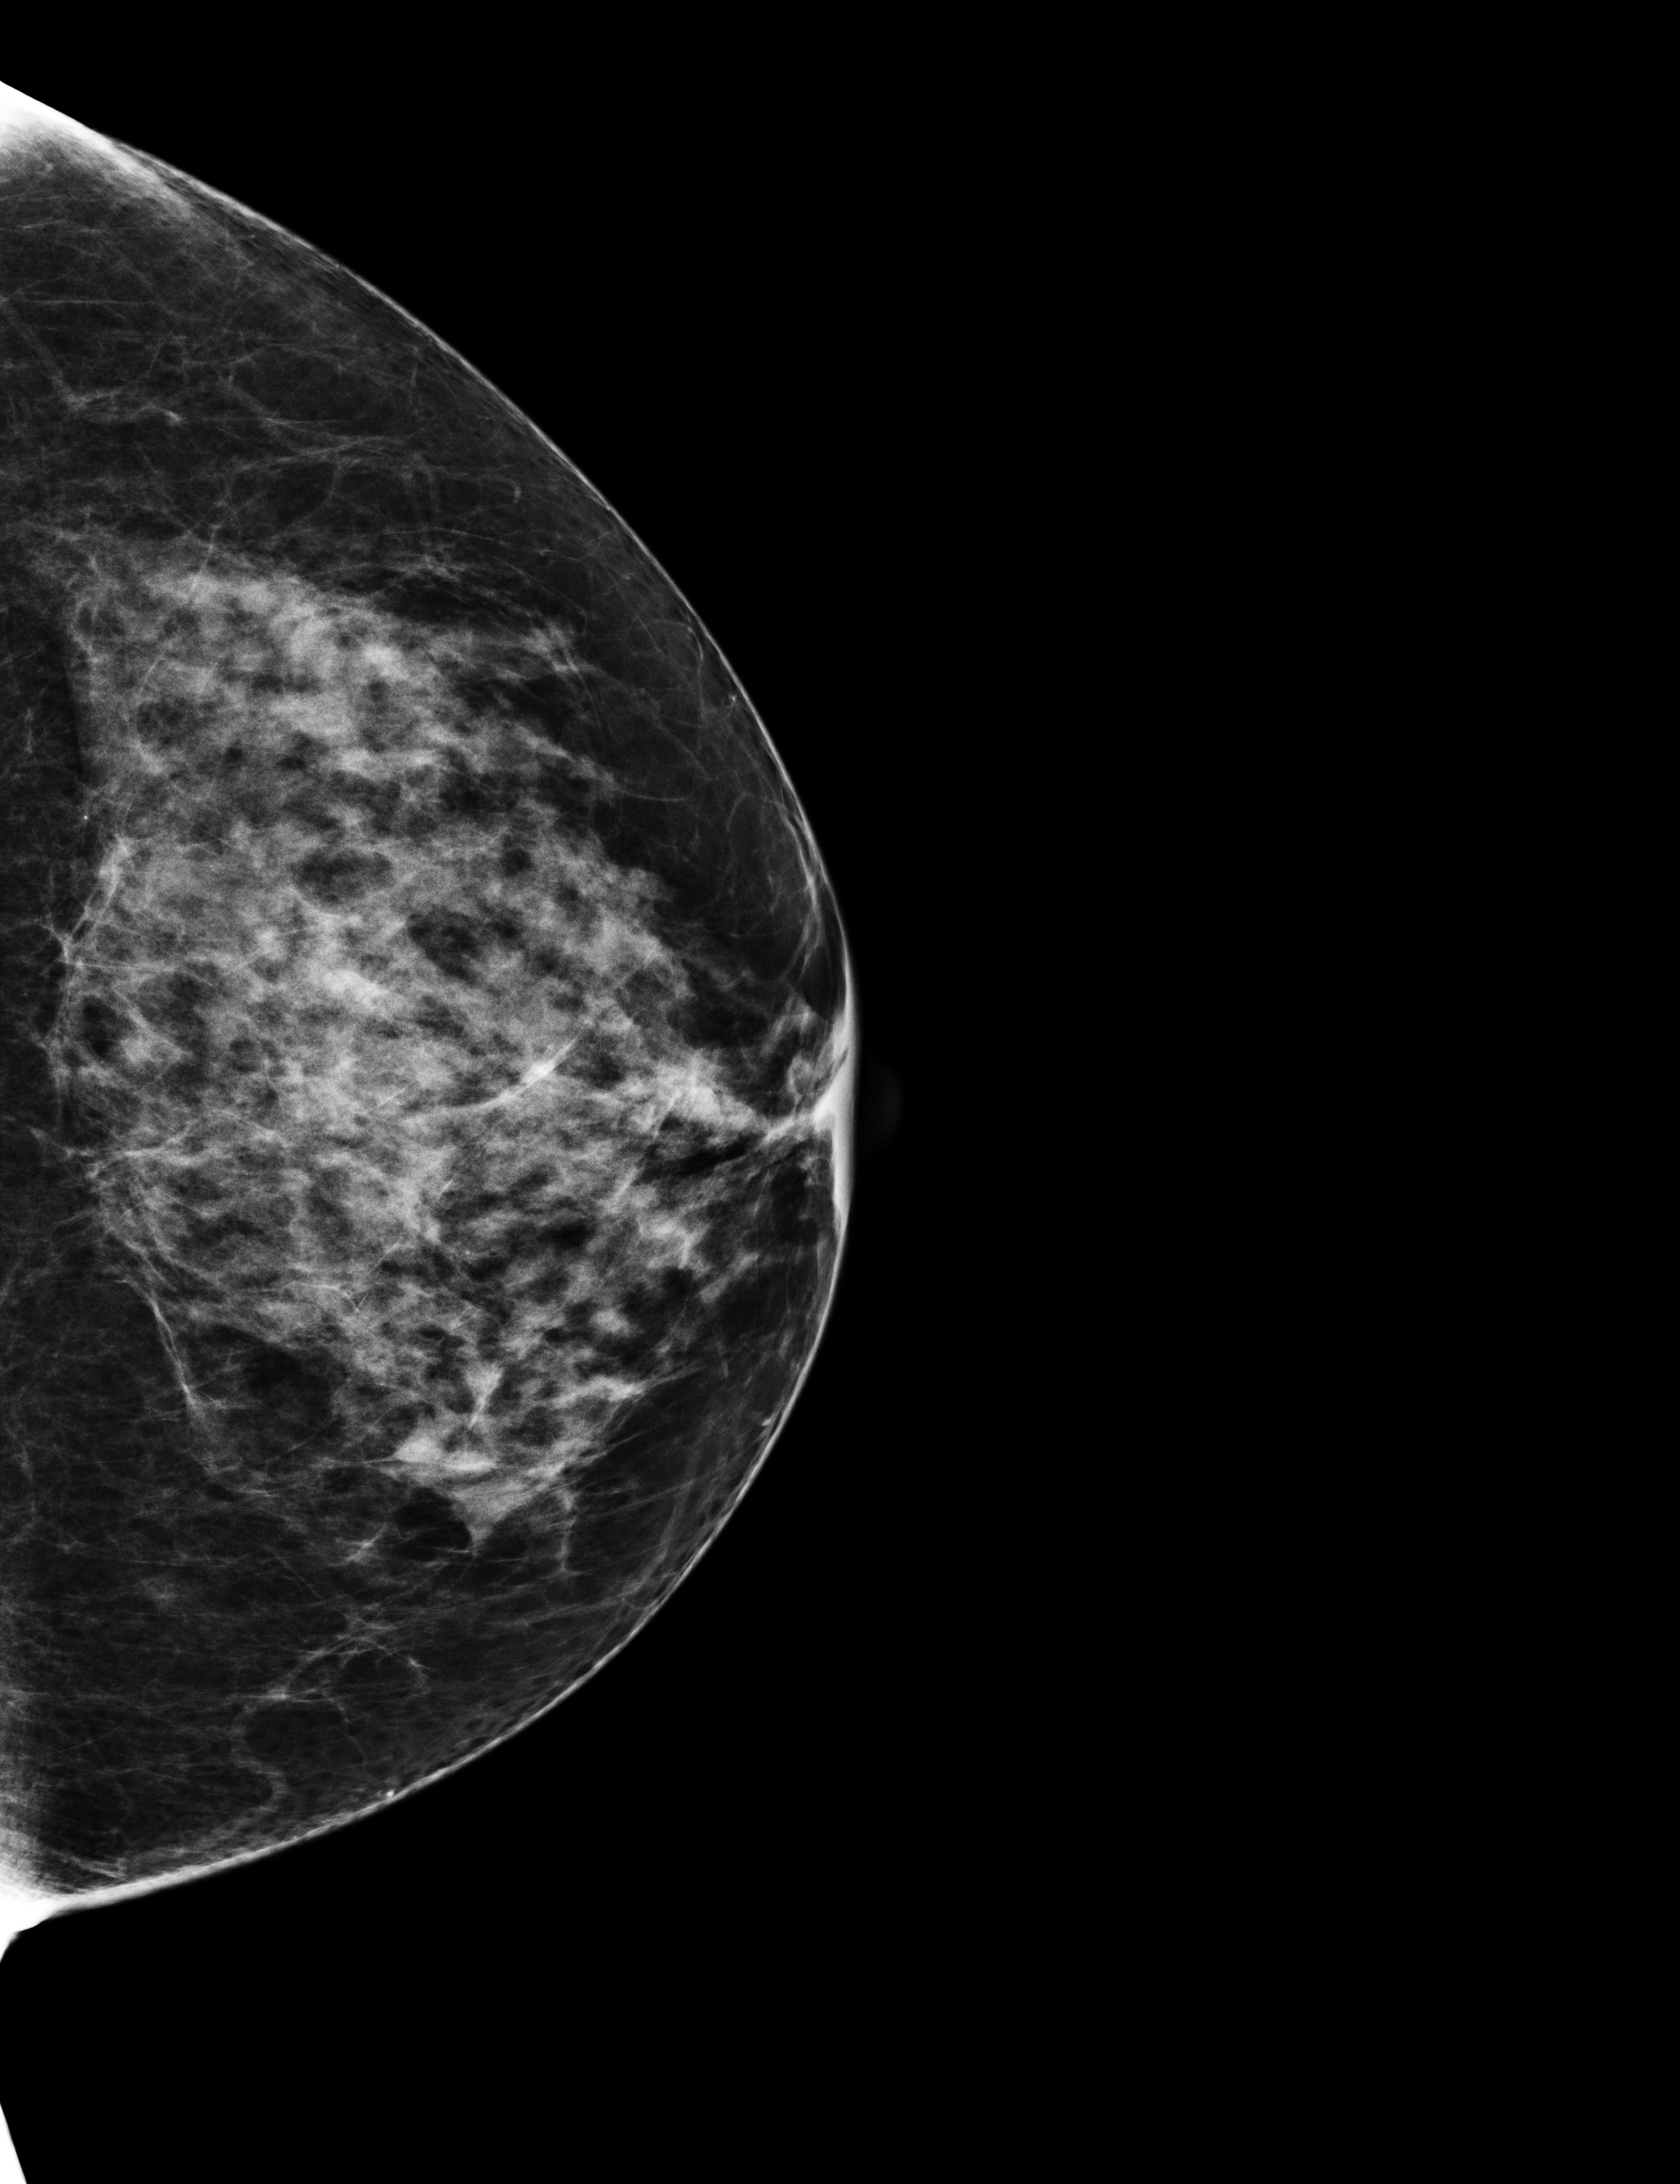
Annual screening mammography examination, compressed breast thickness 55 mm. Patient aged 59 years (female).
Image type: full-field digital mammogram. Breast: left. Projection: craniocaudal (CC) view.